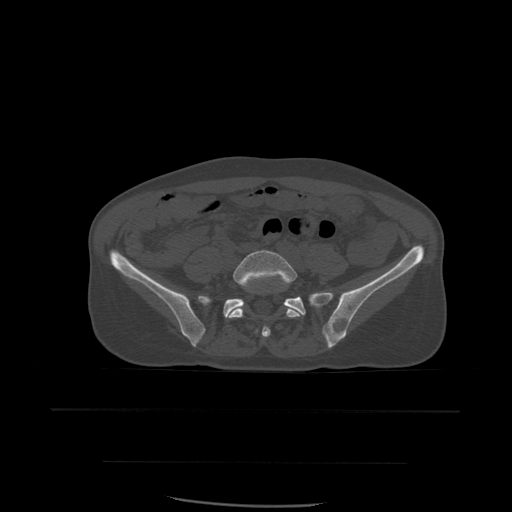
CT including the spine, one axial slice. Bone window (W 1800 / L 400 HU). 1.25 mm slice thickness. 512 × 512 image matrix, field of view 392 × 392 mm. Patient age 48 years. From the clinical record (not read from this slice): primary cancer: lung; vertebrae with lytic lesions (as recorded): T11.
Structures marked on this image (semi-automatically segmented with operator editing):
- L5 vertebra: bounding box [x1, y1, x2, y2] px = [228, 250, 304, 338]